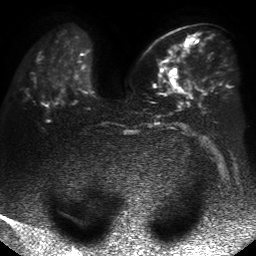
Breast MRI, one axial slice. Position 20 of 50 along the scan axis. Diffusion-weighted series; image 2 of 4 stored at this slice position (different b-values; order by instance number). 1.5 T. 4 mm slice thickness. 256 × 256 image matrix, field of view 360 × 360 mm. Female patient.
Annotated regions visible in this slice (expert manual segmentation):
- tumour on diffusion-weighted imaging: bounding box (x1, y1, x2, y2) in pixels: (169, 68, 176, 77)